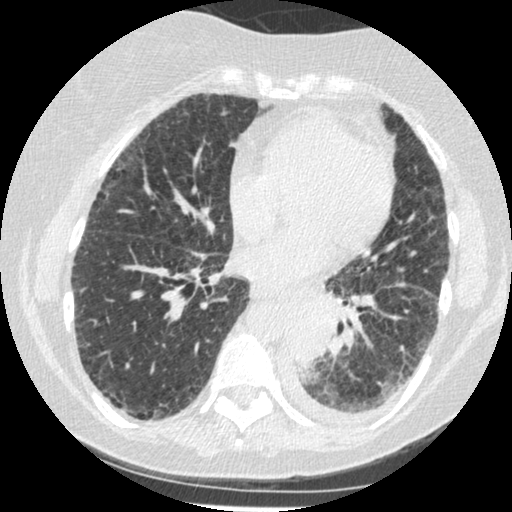
Low-dose screening chest CT, one axial slice; position 93 of 341 along the scan axis; reconstruction kernel STANDARD; 120 kVp; lung window (W 1500 / L -600 HU); 1.25 mm slice thickness; 512 × 512 image matrix, field of view 310 × 310 mm.
Annotated regions visible in this slice (manually delineated by an expert):
- lesion 1 (tumor, lower lobe of left lung): box from (x=289, y=311) to (x=330, y=367) px